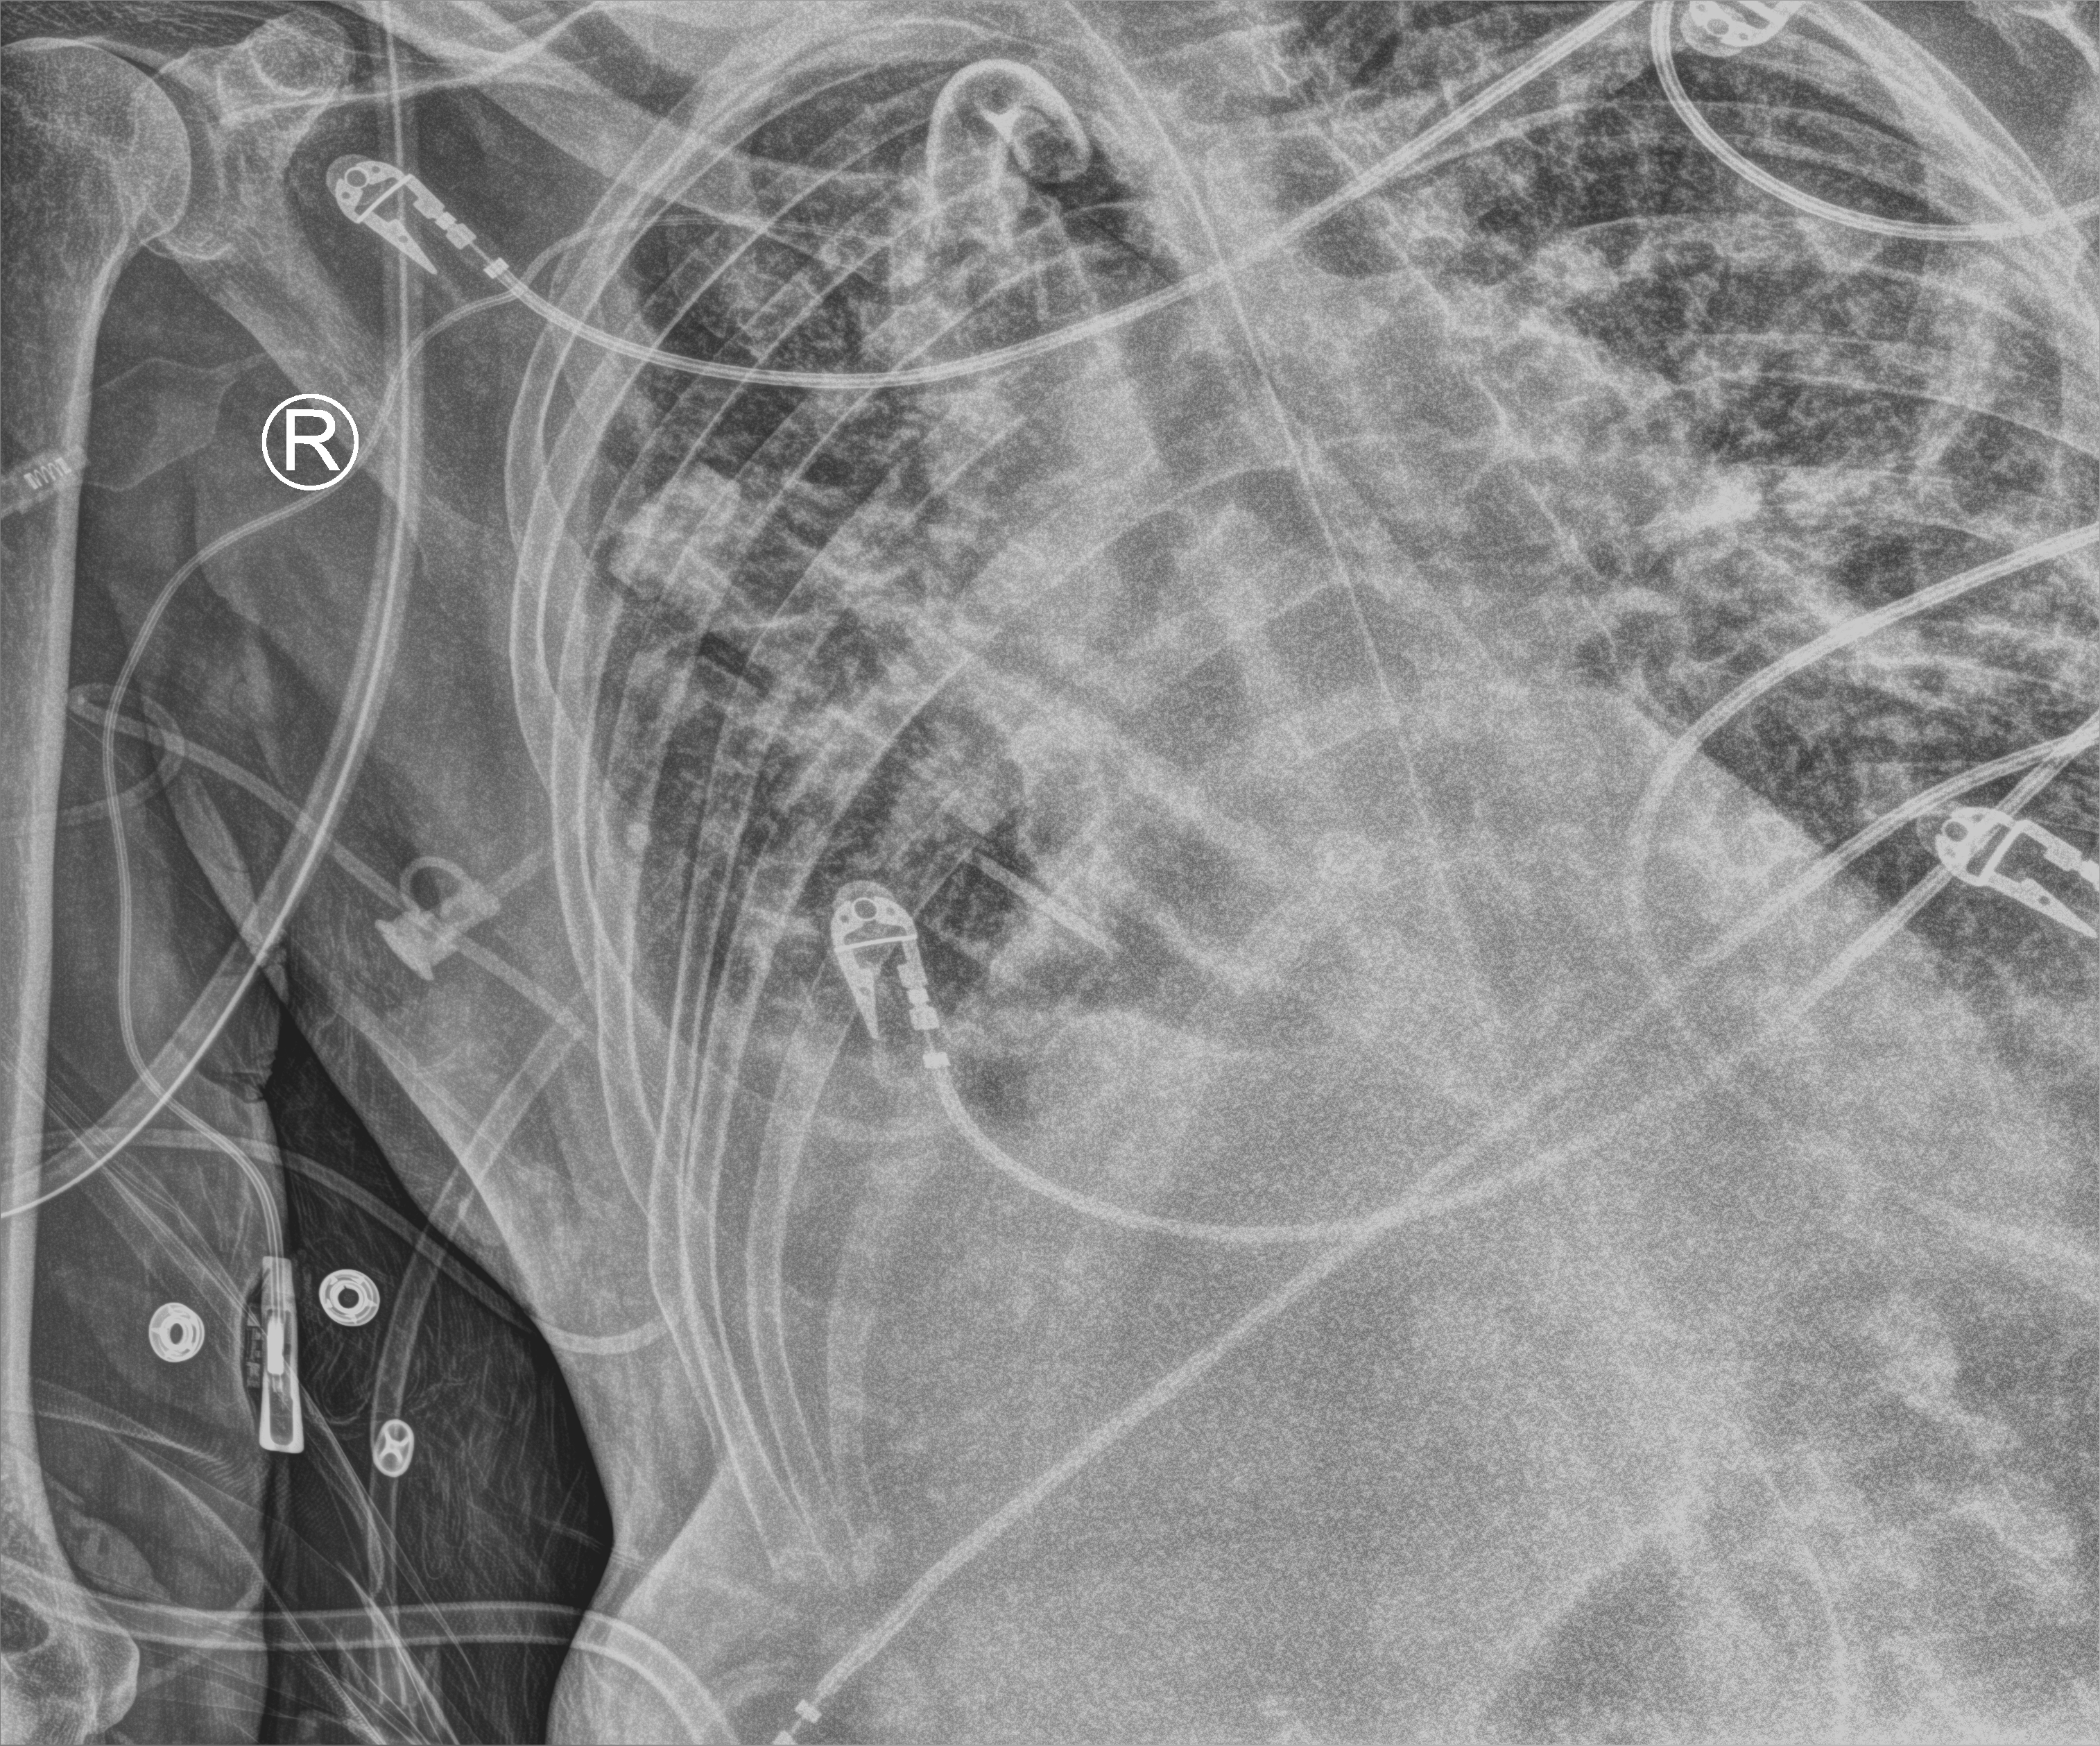
Bedside chest radiograph (computed radiography). Patient hospitalised with COVID-19; male, aged 75–90 years.
Admission-level facts for this patient (not findings on this image; timing relative to this image not recorded):
- length of hospital stay: 70 days
- hypertension (admission record): no
- mechanically ventilated during this hospital stay: yes